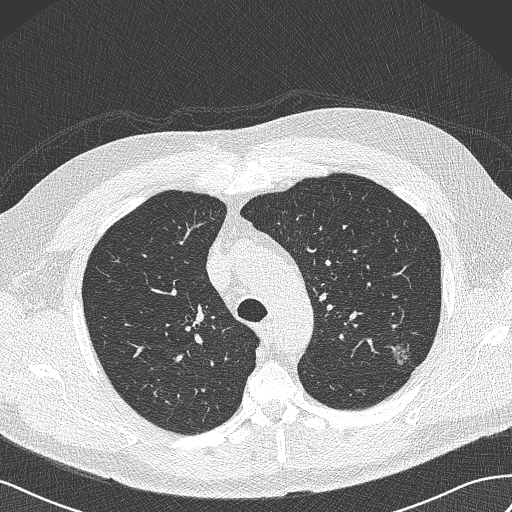
Axial slice from a low-dose chest CT screening exam, baseline annual screen, lung window (W 1500 / L -600 HU), slice 113 of 462 in the series. Male, age 65 years at enrolment. Former smoker at enrolment.
• Lesion marked by an expert reader, bounding box (x1, y1, x2, y2) in pixels: (383, 340, 420, 371).
• The screening reader recorded 3 non-calcified nodules or masses ≥4 mm on this exam (left upper lobe, left upper lobe, right upper lobe); which of them this box marks is not recorded.
• Participant outcome: lung cancer diagnosed 541 days after this screen — adenocarcinoma, NOS, left upper lobe, poorly differentiated (G3), stage IA (AJCC 6th edition), 13 mm at pathology.